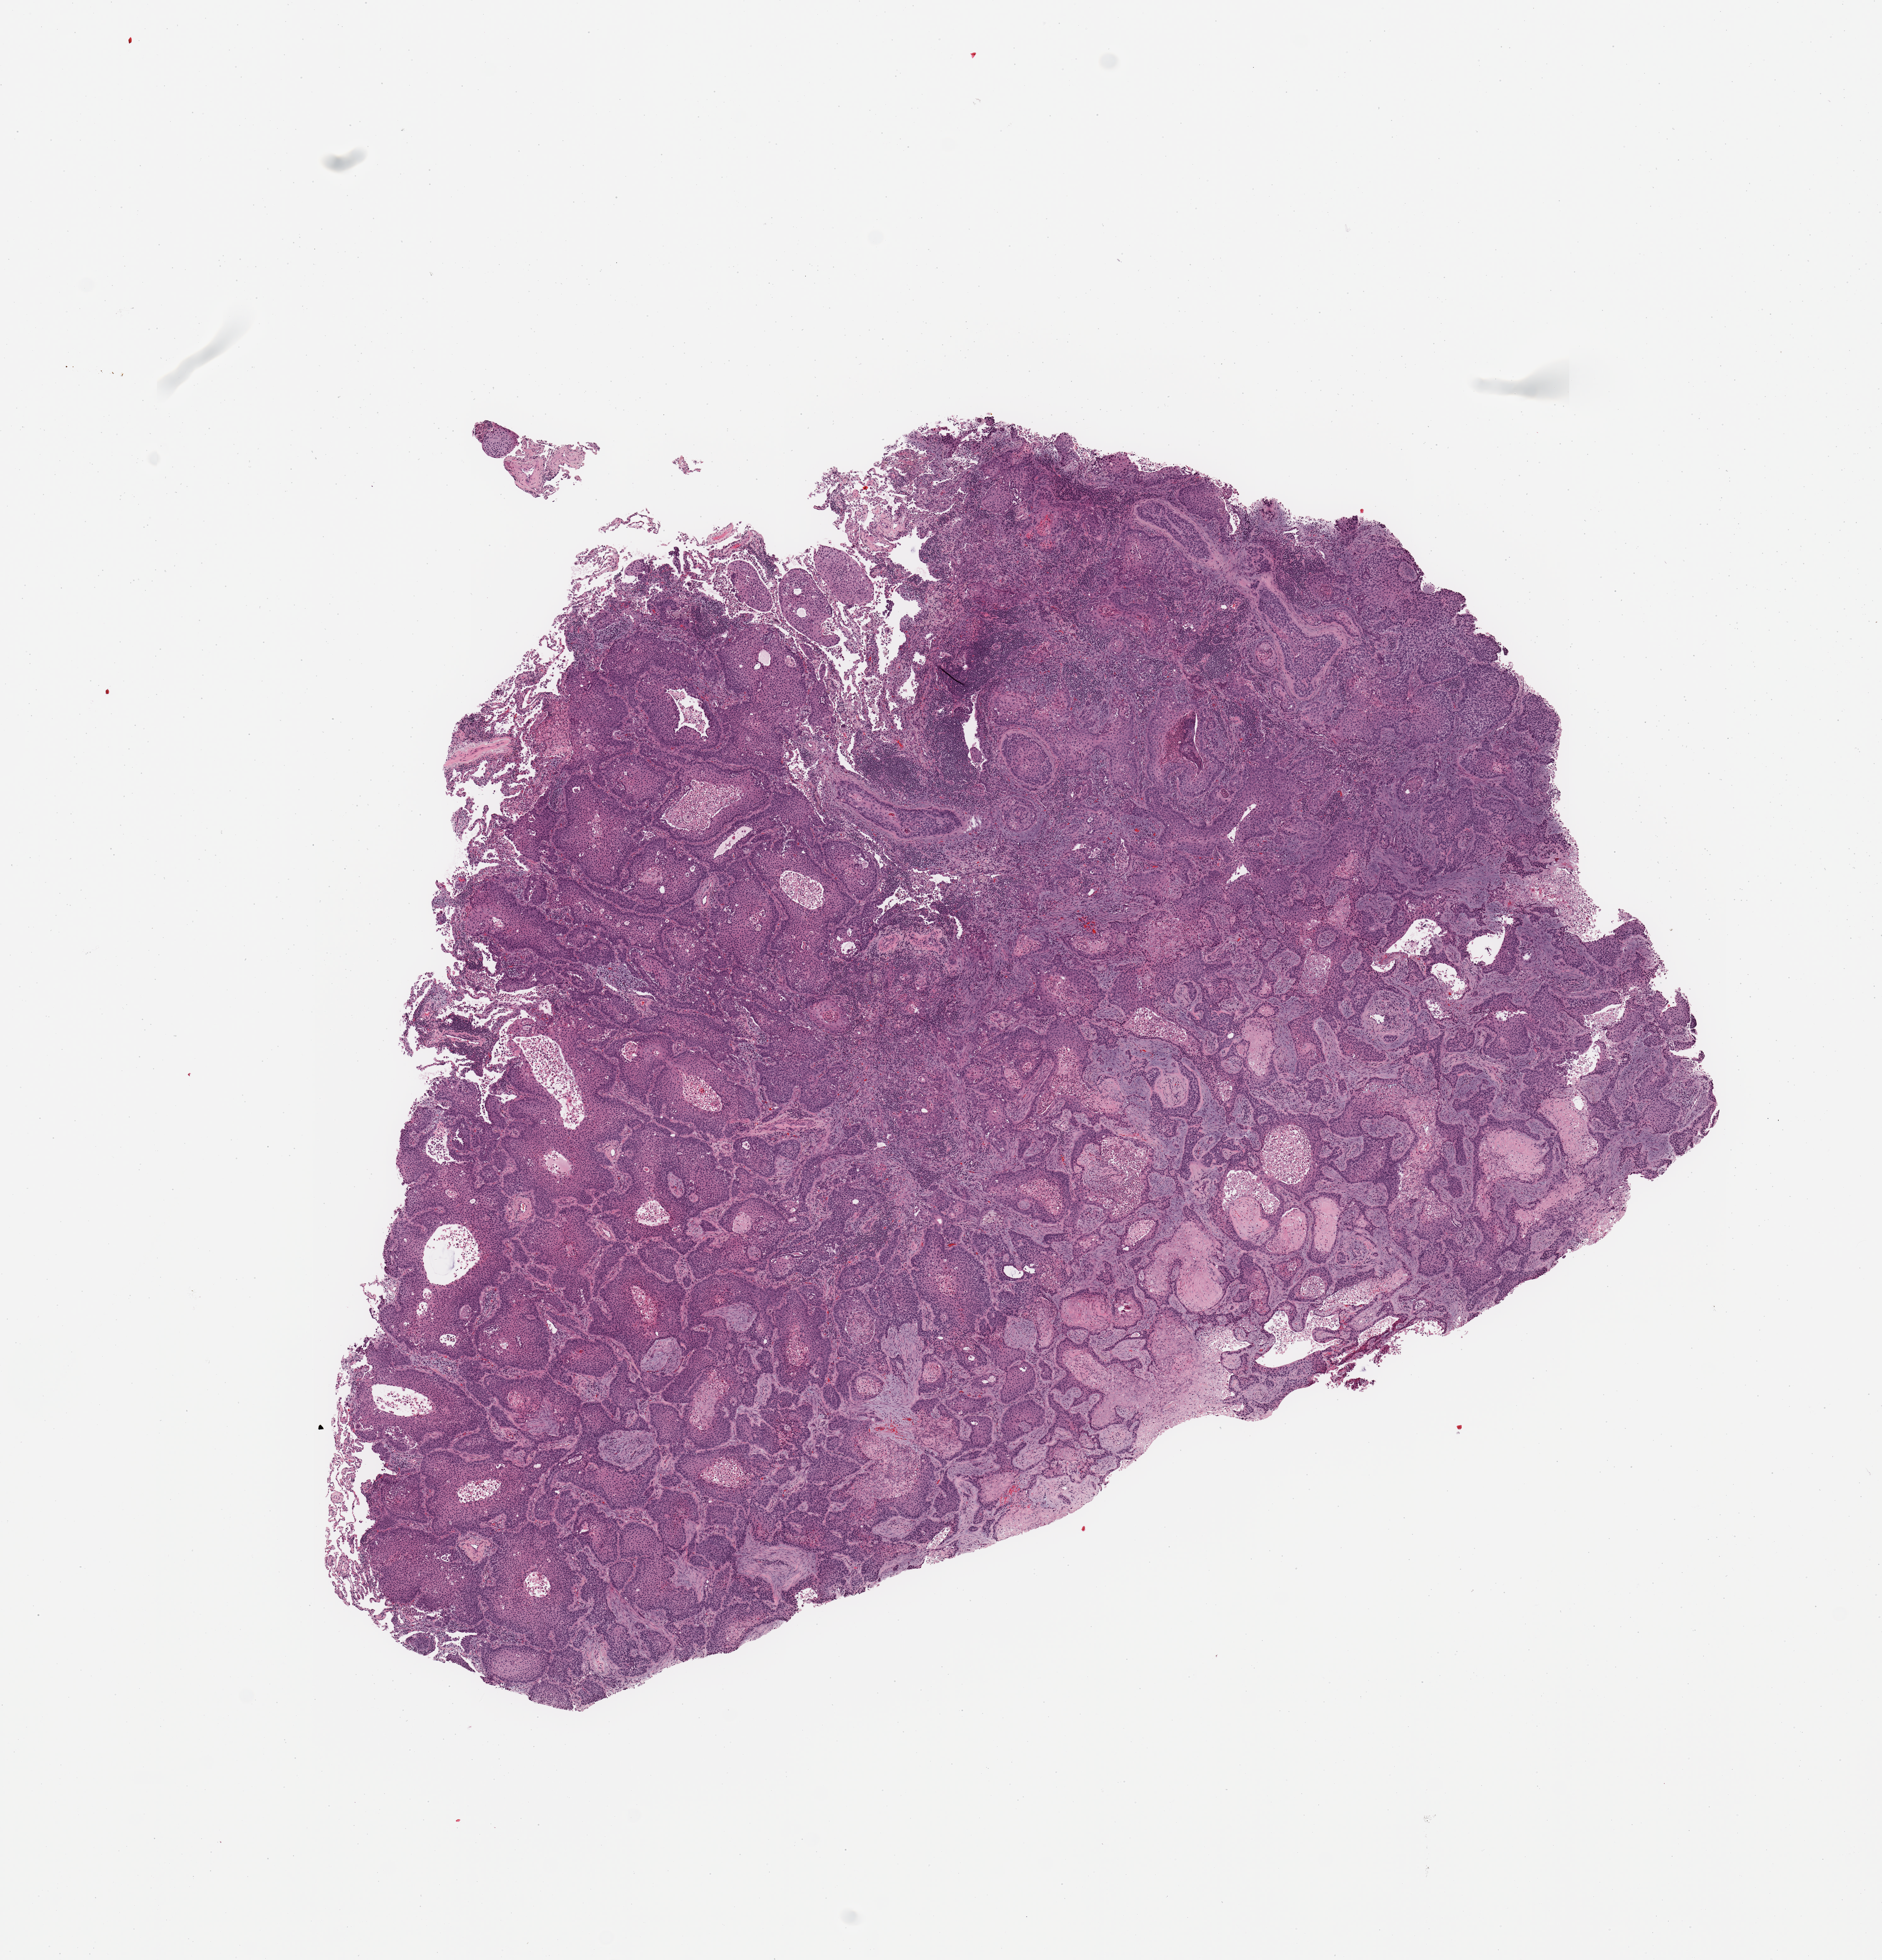
Digitized Hematoxylin and eosin (H&E) stained tissue section (whole slide), low-resolution overview of the scanned area, about 11.8 x 12.3 mm (from a 20x scan). Tumour tissue sample, sampled site: lung. 75-year-old female patient. Composition of this section per pathologist review: tumour nuclei 75%, necrosis 5%.
Histologic diagnosis: Squamous cell carcinoma, NOS.